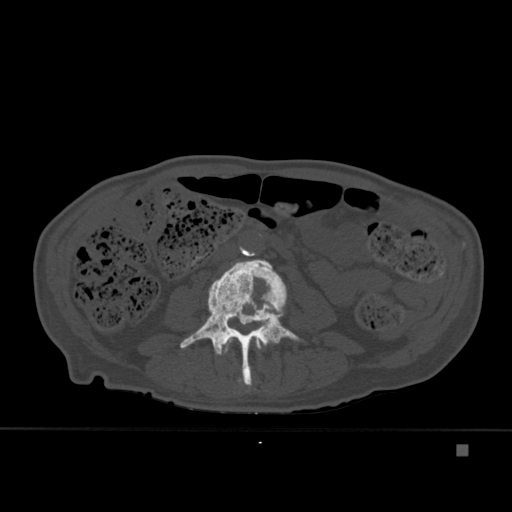
CT including the spine, one axial slice; position 143 of 451 along the scan axis; bone window (W 1800 / L 400 HU); 1.5 mm slice thickness; 512 × 512 image matrix, field of view 378 × 378 mm. Male patient, age 75 years. From the clinical record (not read from this slice): primary cancer: prostate.
Annotated regions visible in this slice (semi-automatic segmentation, software-assisted and operator-edited):
- L2 vertebra: bounding box <221,337,261,384> (left, top, right, bottom; pixels)
- L3 vertebra: <180,259,300,388>